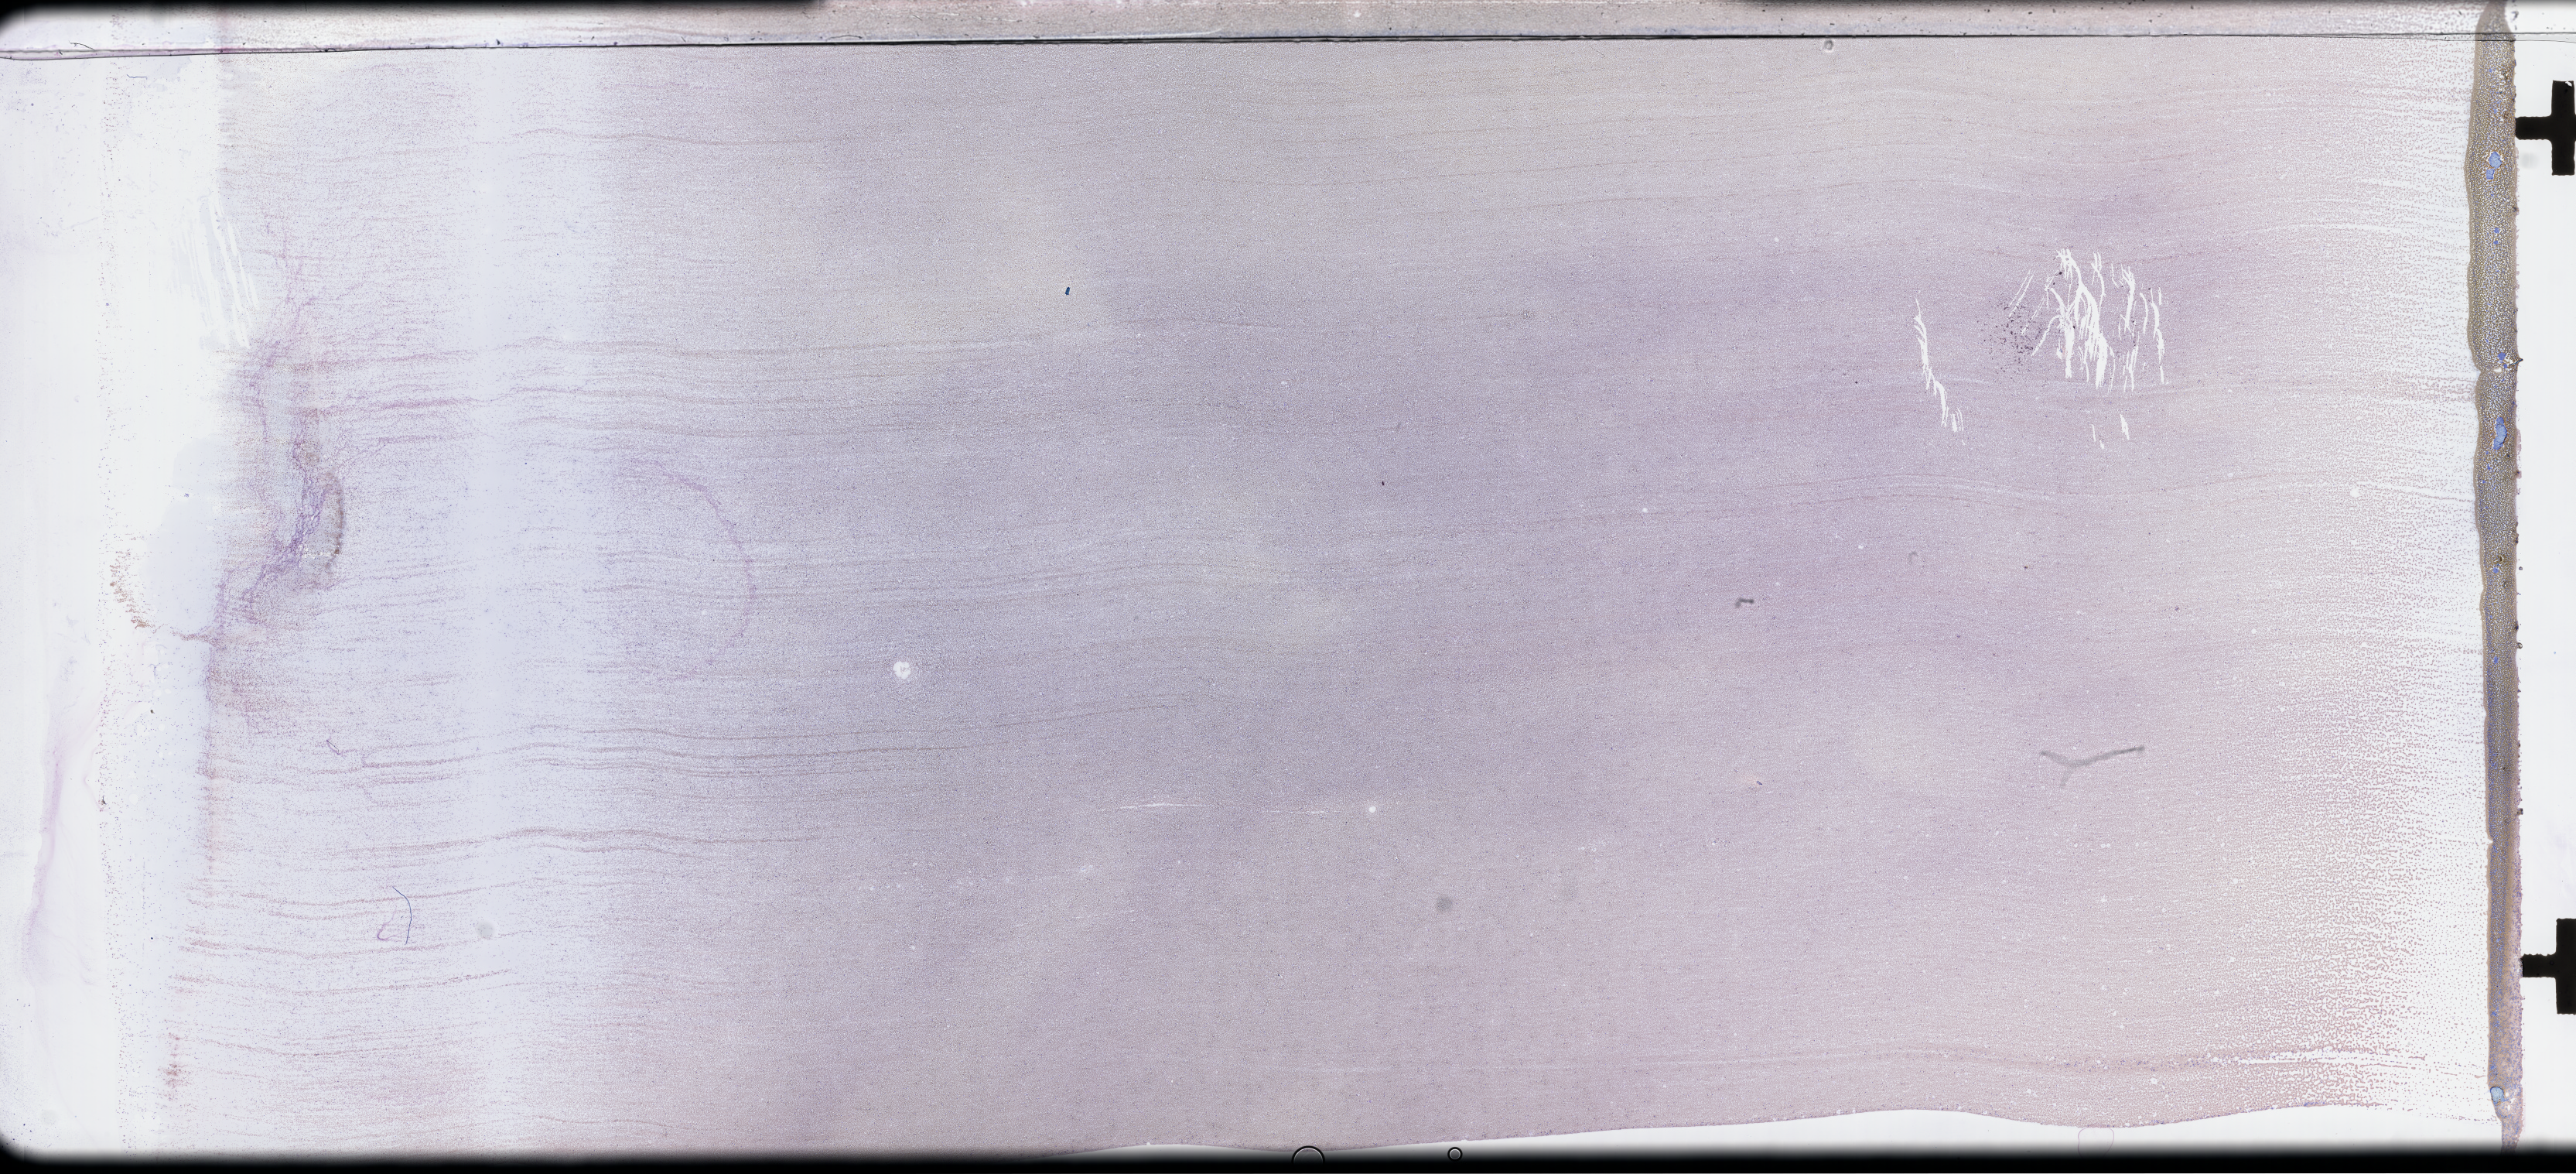
Whole-slide image of a whole blood smear, Wright–Giemsa stain, a low-resolution overview of the entire scanned area, about 53.8 x 24.5 mm; smear from an EDTA sample. Patient sex: male.
* patient diagnosis: Plasma Cell Myeloma